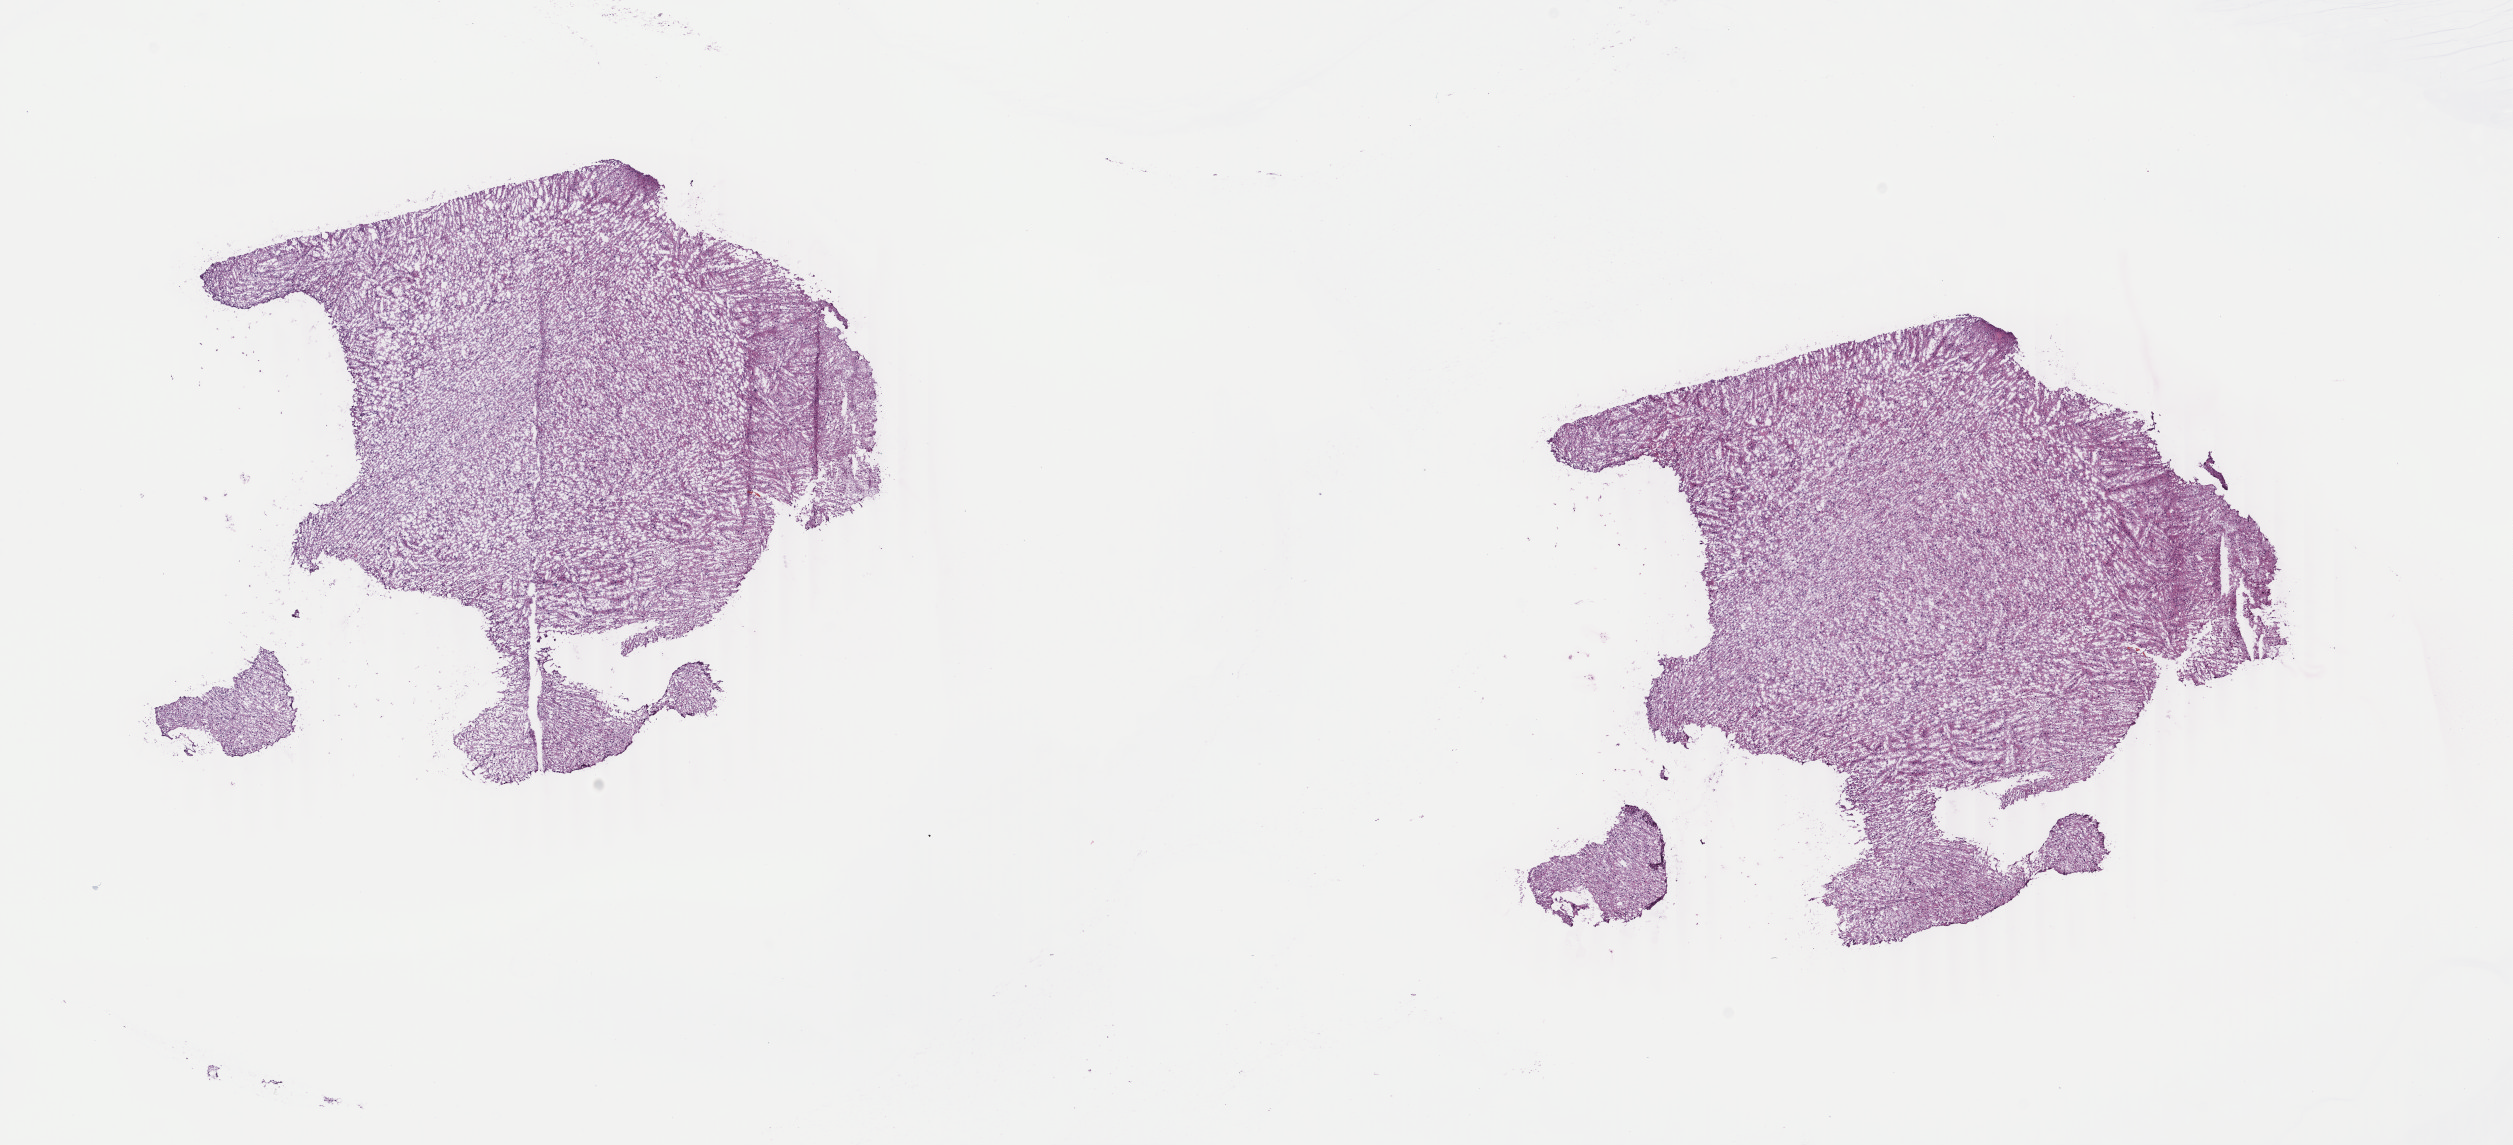
H&E-stained whole-slide image, a low-resolution overview of the entire scanned area, about 20.0 x 9.1 mm. Frozen section from the top of the tissue portion. Brain, primary tumour sample. Patient: female, age at initial diagnosis 24 years. Histologic grade: G2 (moderately differentiated). Pathologist review of this section (percent, as recorded): tumour cells 40%, tumour nuclei 80%, normal cells 10%, stromal cells 50%, necrosis 0%. Inflammatory infiltration, as recorded: lymphocyte infiltration 0%, monocyte infiltration 0%, neutrophil infiltration 0%.
Pathologic diagnosis: Astrocytoma, NOS (cerebrum).